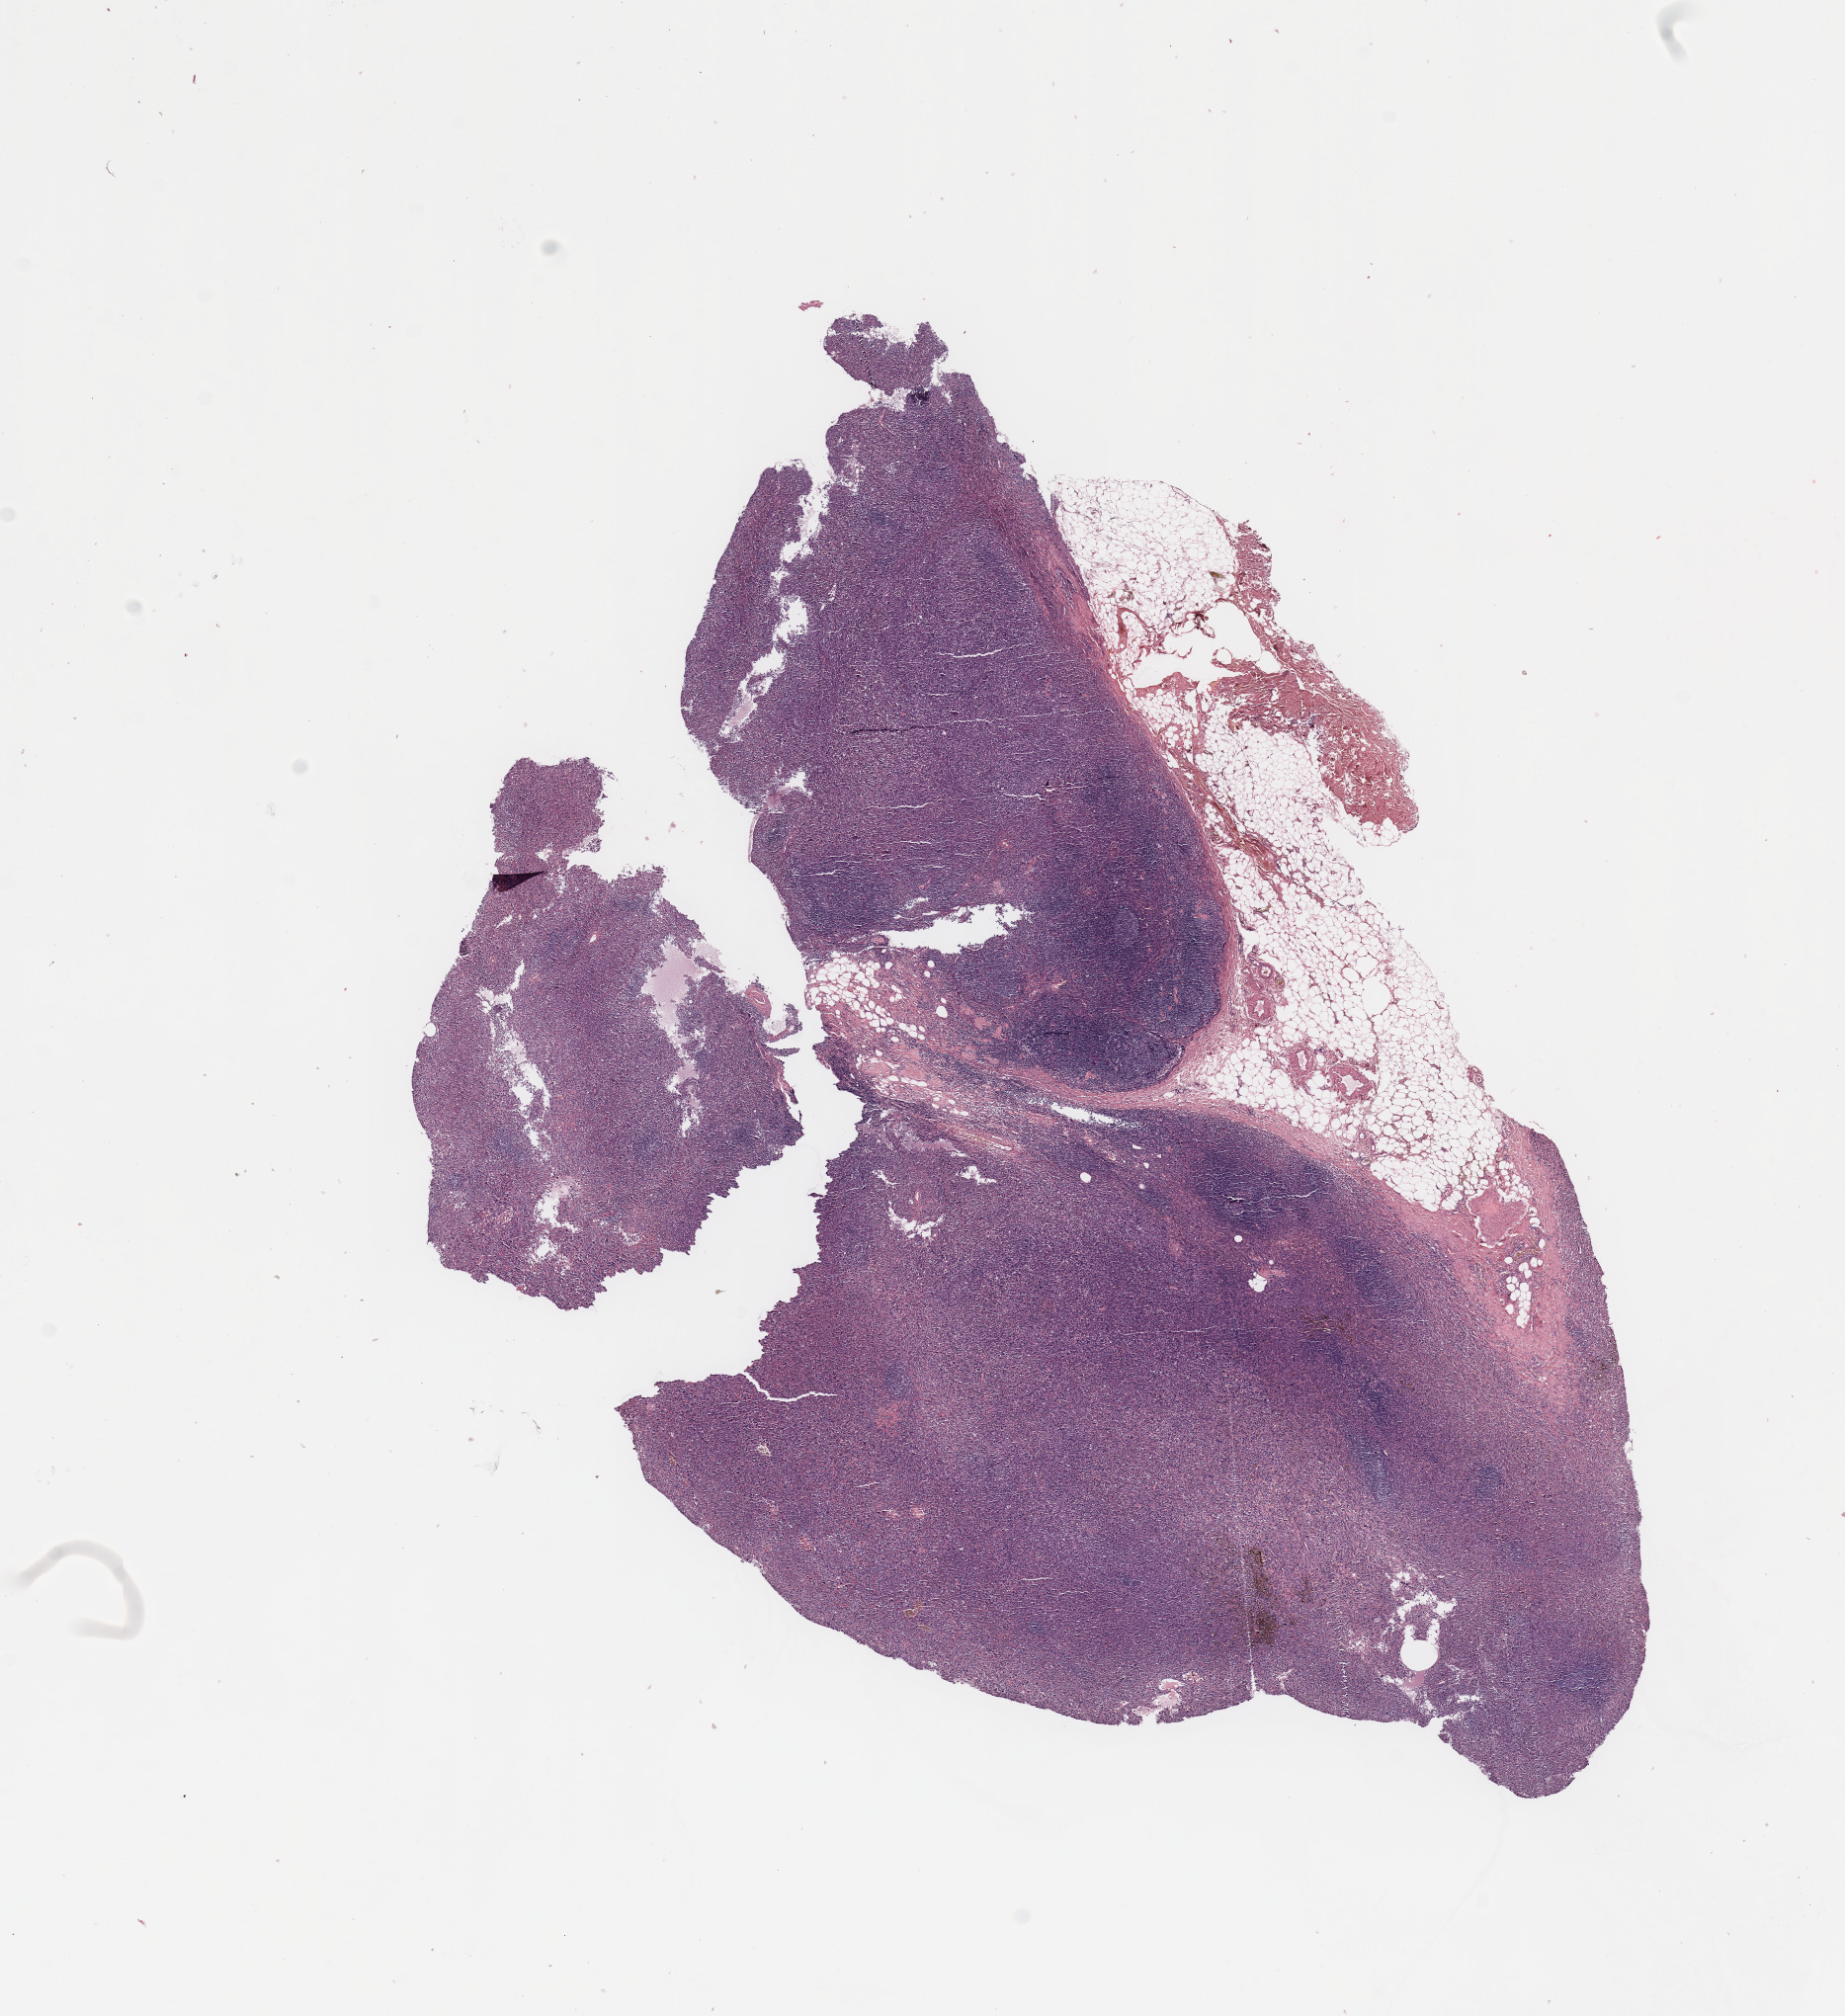
Digitized H&E tissue section (whole slide), whole scanned area (about 14.8 x 16.1 mm, slide scanned at 20x) shown as a low-resolution overview, melanoma tumour tissue; sampled site not recorded. Patient: male, age 77 years.
• AJCC pathologic stage: IA
• diagnosis: Malignant melanoma, NOS